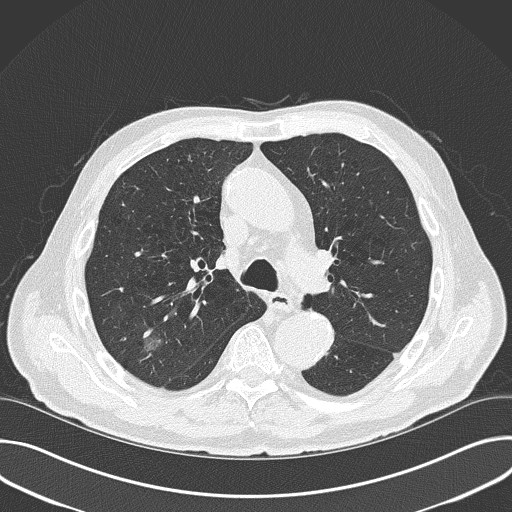
Low-dose screening chest CT, one axial slice; slice 109 of 177 in the series (ordered by position); reconstruction kernel B50f; lung window (W 1500 / L -600 HU); 512 × 512 image matrix.
Outlined on this slice (manually delineated by an expert):
- lesion 1 (tumor, upper lobe of right lung): bounding box <143,336,164,351> (left, top, right, bottom; pixels)